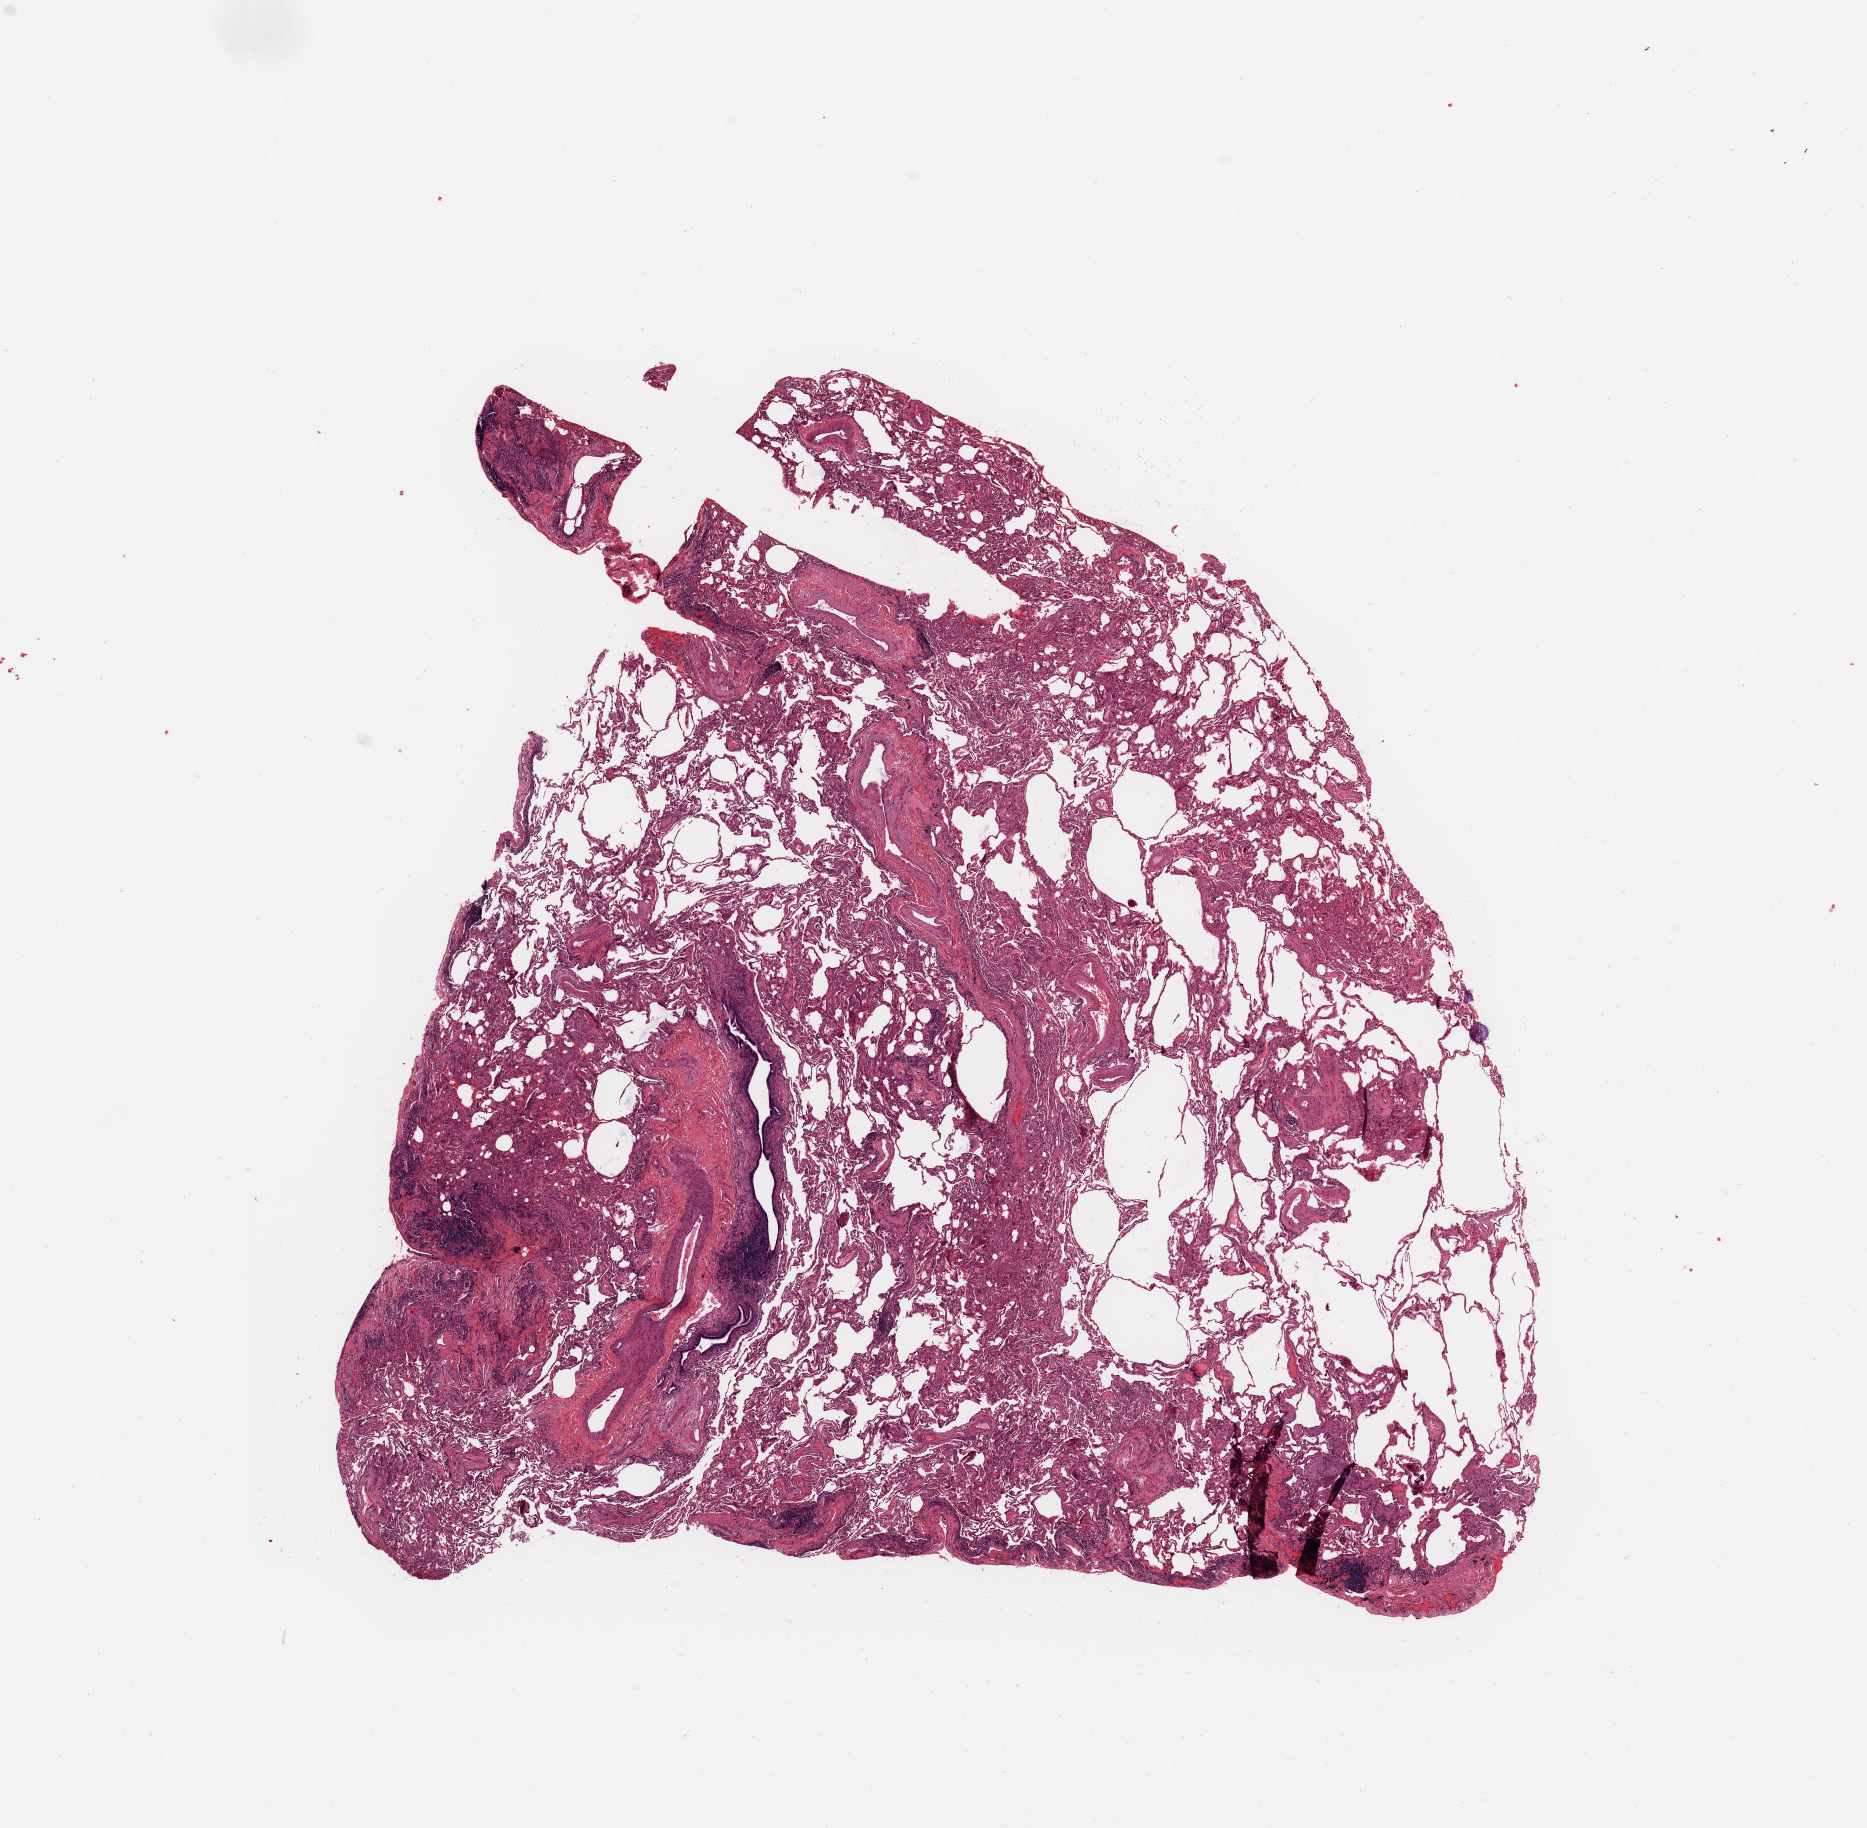
Whole-slide histology image, H&E-stained — a low-resolution overview of the entire scanned area, about 14.8 x 14.5 mm. Normal (non-tumour) tissue sample, lung. Male, 88 y/o.
This section: normal (non-tumour) tissue from the same patient. Patient diagnosis: Squamous cell carcinoma, NOS.